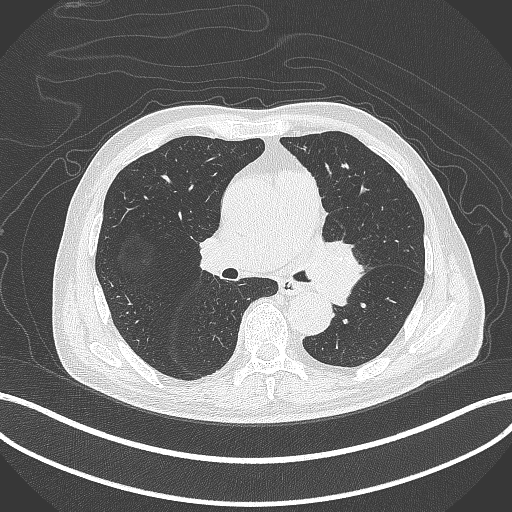
Chest CT, one axial slice. Position 244 of 417 along the scan axis. Reconstruction kernel B70f. 120 kVp. Lung window (W 1500 / L -600 HU). 1 mm slice thickness. 512 × 512 image matrix. Patient: male, 77 years. Case-level facts recorded for this patient, not image findings: clinical TNM (as recorded): T3 N1 M0.
Annotated regions visible in this slice (bounding box drawn by a radiologist):
- lung tumour (recorded histology: adenocarcinoma): bounding box (x1, y1, x2, y2) in pixels: (307, 234, 366, 303)